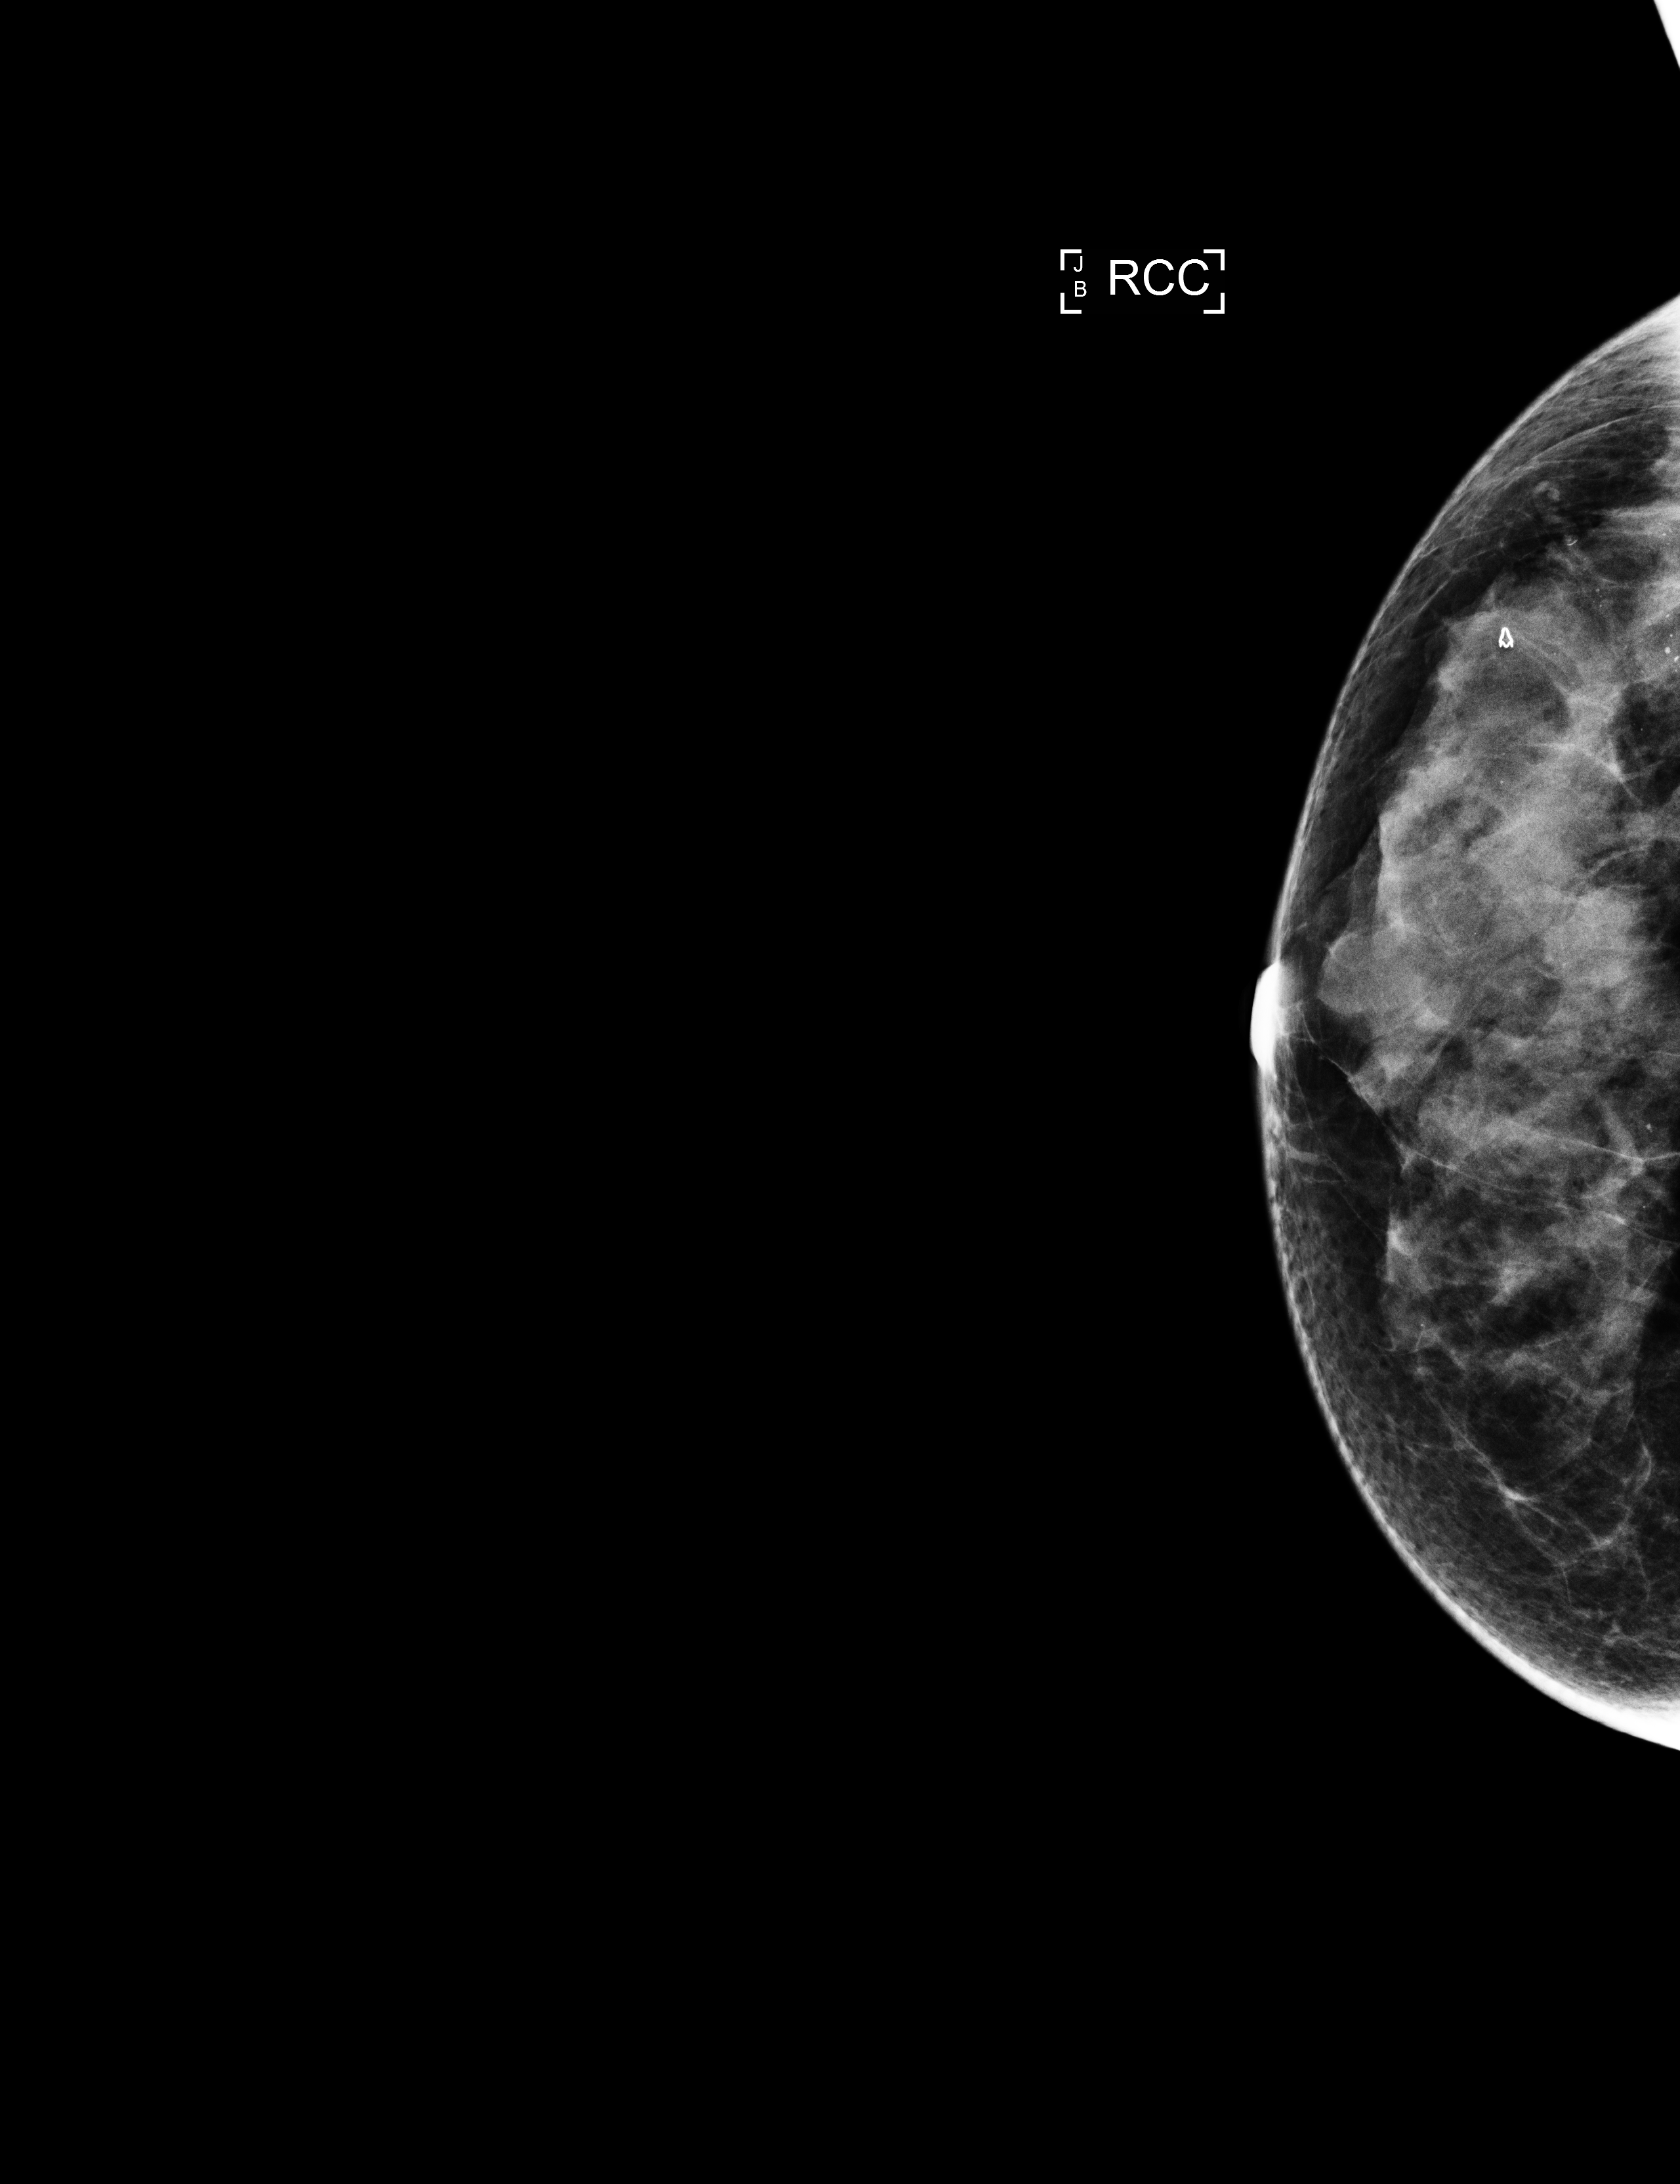
Digital mammogram (FFDM); right breast; CC view; screening examination; compressed breast thickness 41 mm. Female patient, age 58 years.
Breast density at the screening exam (both breasts): heterogeneously dense (BI-RADS density category c). Final BI-RADS assessment for this screening round (tomosynthesis exam, both breasts): category 1. Recall: no recall after this screen.